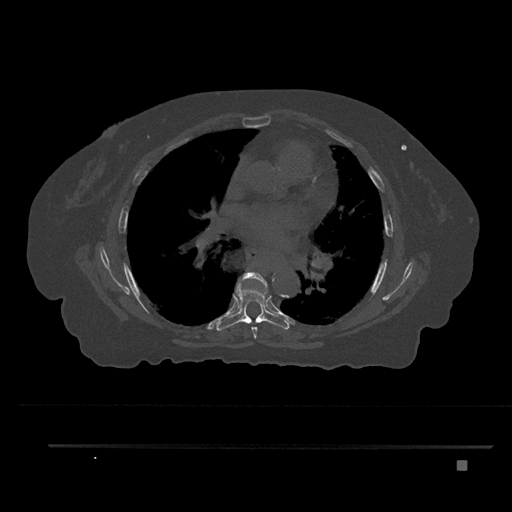
CT including the spine, one axial slice; position 499 of 797 along the scan axis; 120 kVp; bone window (W 1800 / L 400 HU); 0.5 mm slice thickness; 512 × 512 image matrix, field of view 437 × 437 mm. Patient: female, 76 years. Case-level facts recorded for this patient, not image findings: primary cancer: lung.
Outlined on this slice (semi-automatically segmented with operator editing):
- T6 vertebra: bounding box <238,272,268,339> (left, top, right, bottom; pixels)
- T7 vertebra: <216,282,290,331>